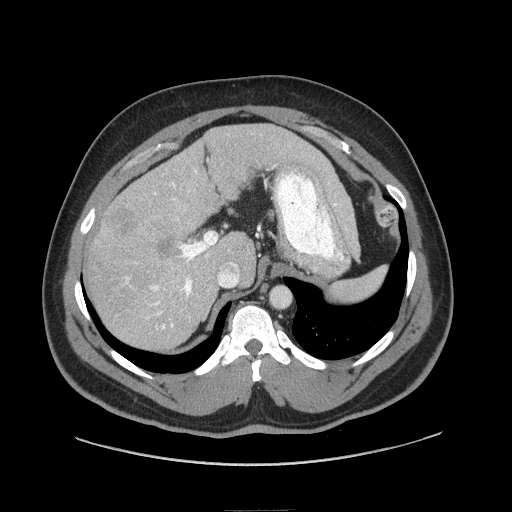
Contrast-enhanced abdominal CT (liver protocol), one axial slice. Slice 54 of 87 in the series (ordered by position). Reconstruction kernel STANDARD. Soft-tissue window (W 400 / L 40 HU). 512 × 512 image matrix. Case-level facts recorded for this patient, not image findings: diagnosis: hepatocellular carcinoma (patient treated with transarterial chemoembolisation; whether this scan precedes or follows treatment is not stated here); TNM stage (as recorded): Stage-II; Child-Pugh class: A; tumour differentiation: moderately differentiated; tumour nodularity: uninodular.
Outlined on this slice (semi-automatic segmentation, software-assisted and operator-edited):
- liver parenchyma outside the tumour (the mass and vessels are separate outlines, so this box may not span the whole liver): bounding box [x1, y1, x2, y2] px = [84, 124, 328, 350]
- mass: [102, 200, 180, 264]
- liver vessels: [126, 171, 237, 329]